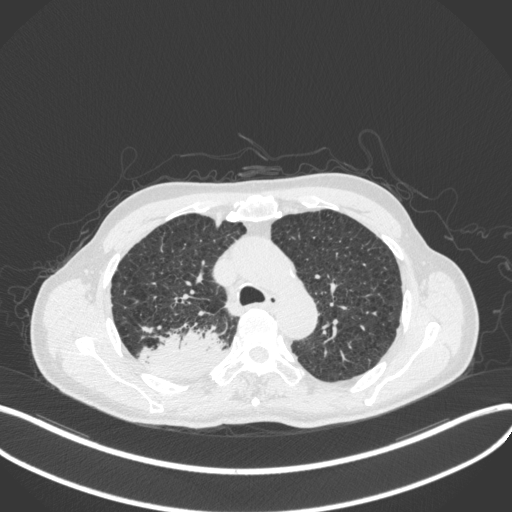
Chest CT, one axial slice. Position 324 of 423 along the scan axis. 120 kVp. Lung window (W 1500 / L -600 HU). 1 mm slice thickness. 512 × 512 image matrix. Male patient, age 79 years. From the clinical record (not read from this slice): clinical TNM (as recorded): T3 N0 M0.
Annotated regions visible in this slice (bounding box drawn by a radiologist):
- lung tumour (recorded histology: adenocarcinoma): bounding box <136,327,226,380> (left, top, right, bottom; pixels)